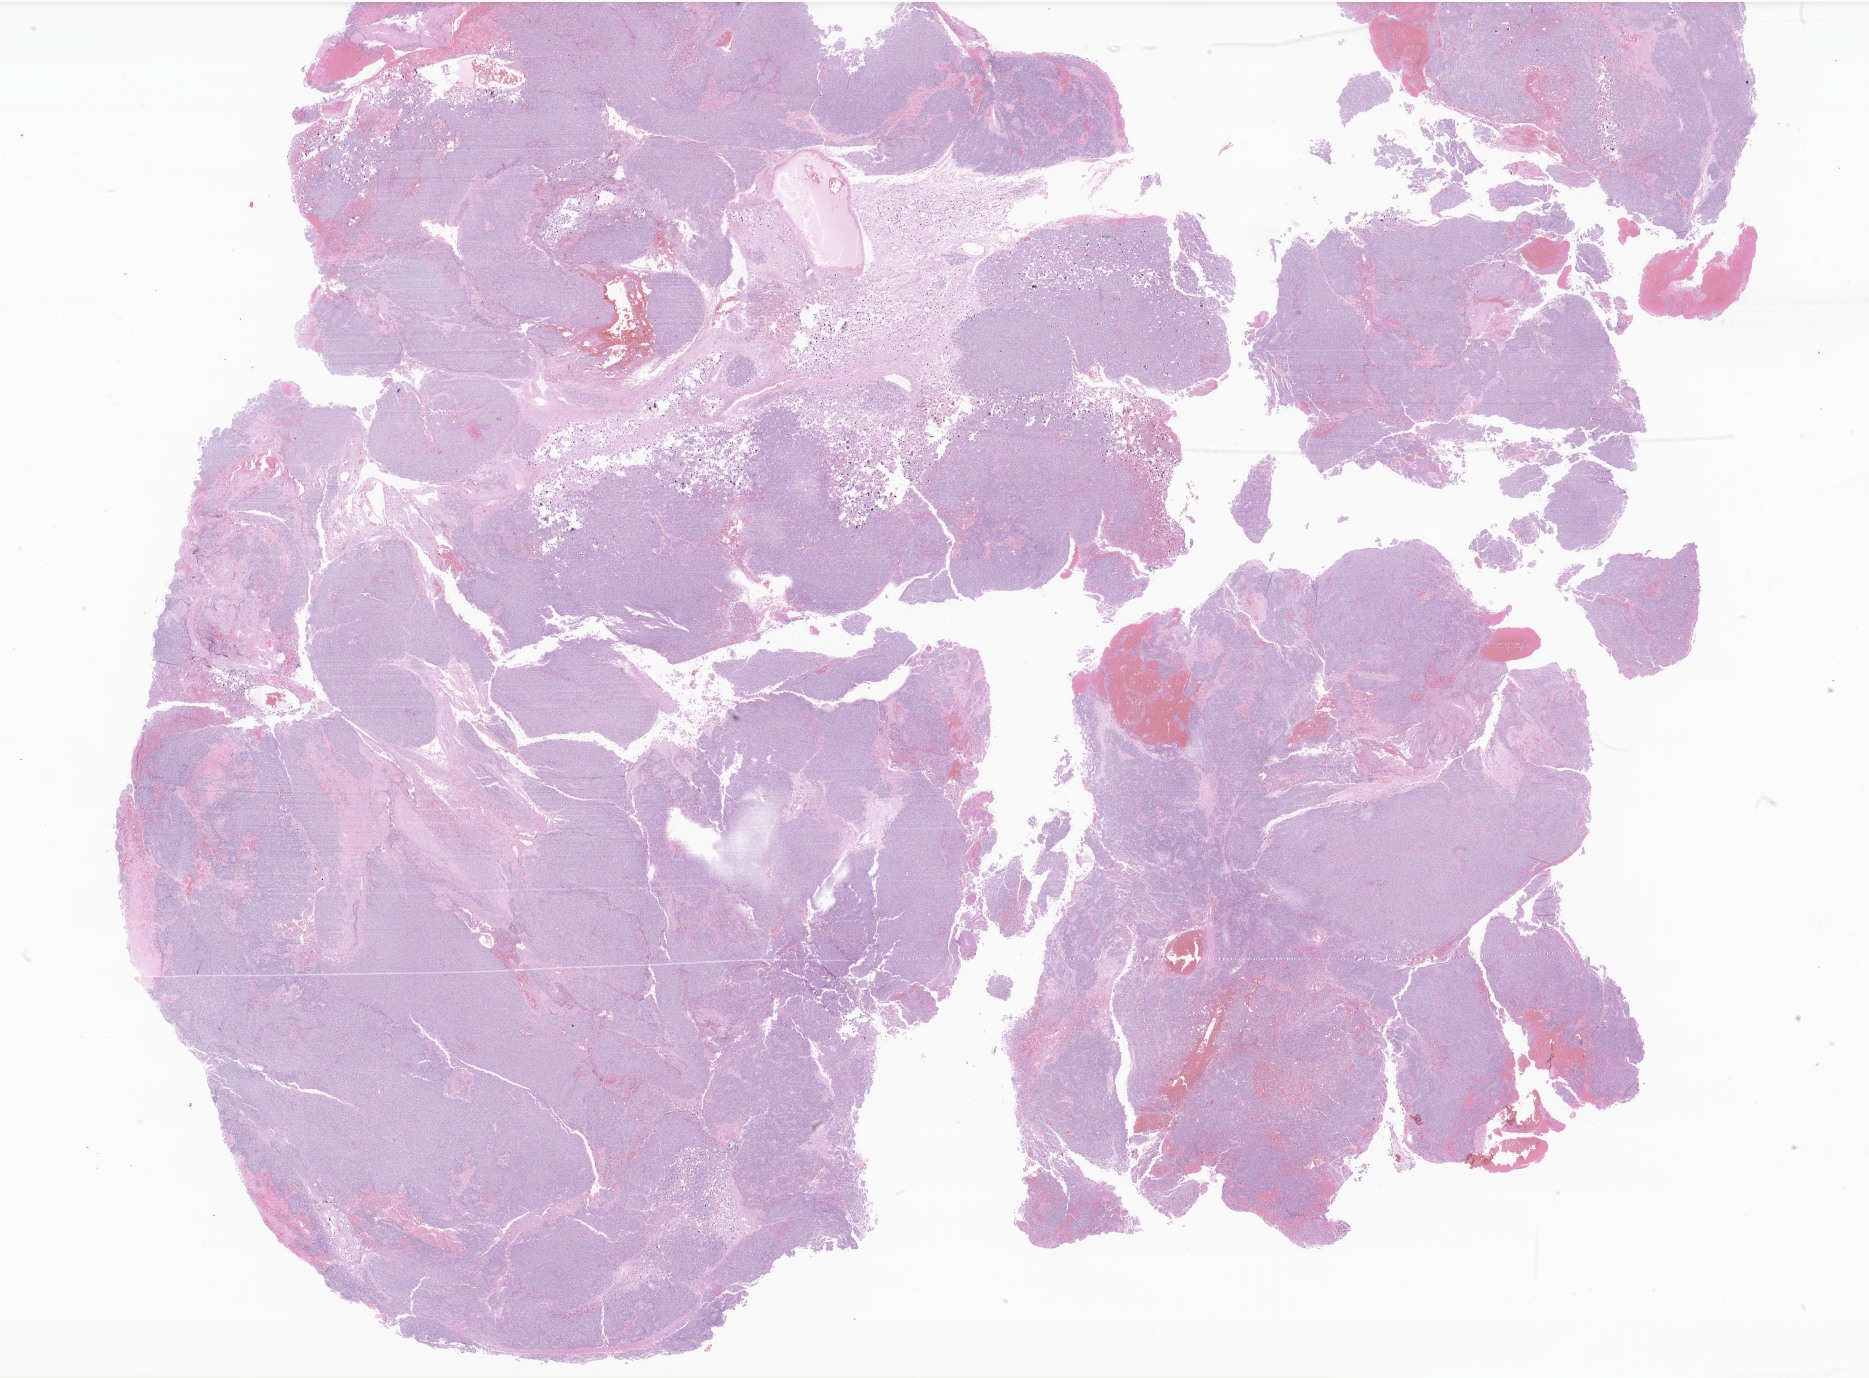
Whole-slide image, haematoxylin and eosin stain of tumor tissue from the brain, shown as a low-resolution overview of the whole scanned area (about 31.5 x 23.2 mm). Formalin-fixed, paraffin-embedded (FFPE) tissue. Patient: male, age 193 months (16 years 1 month).
Diagnosis (ICD-O-3 morphology term): Neoplasm, uncertain whether benign or malignant.